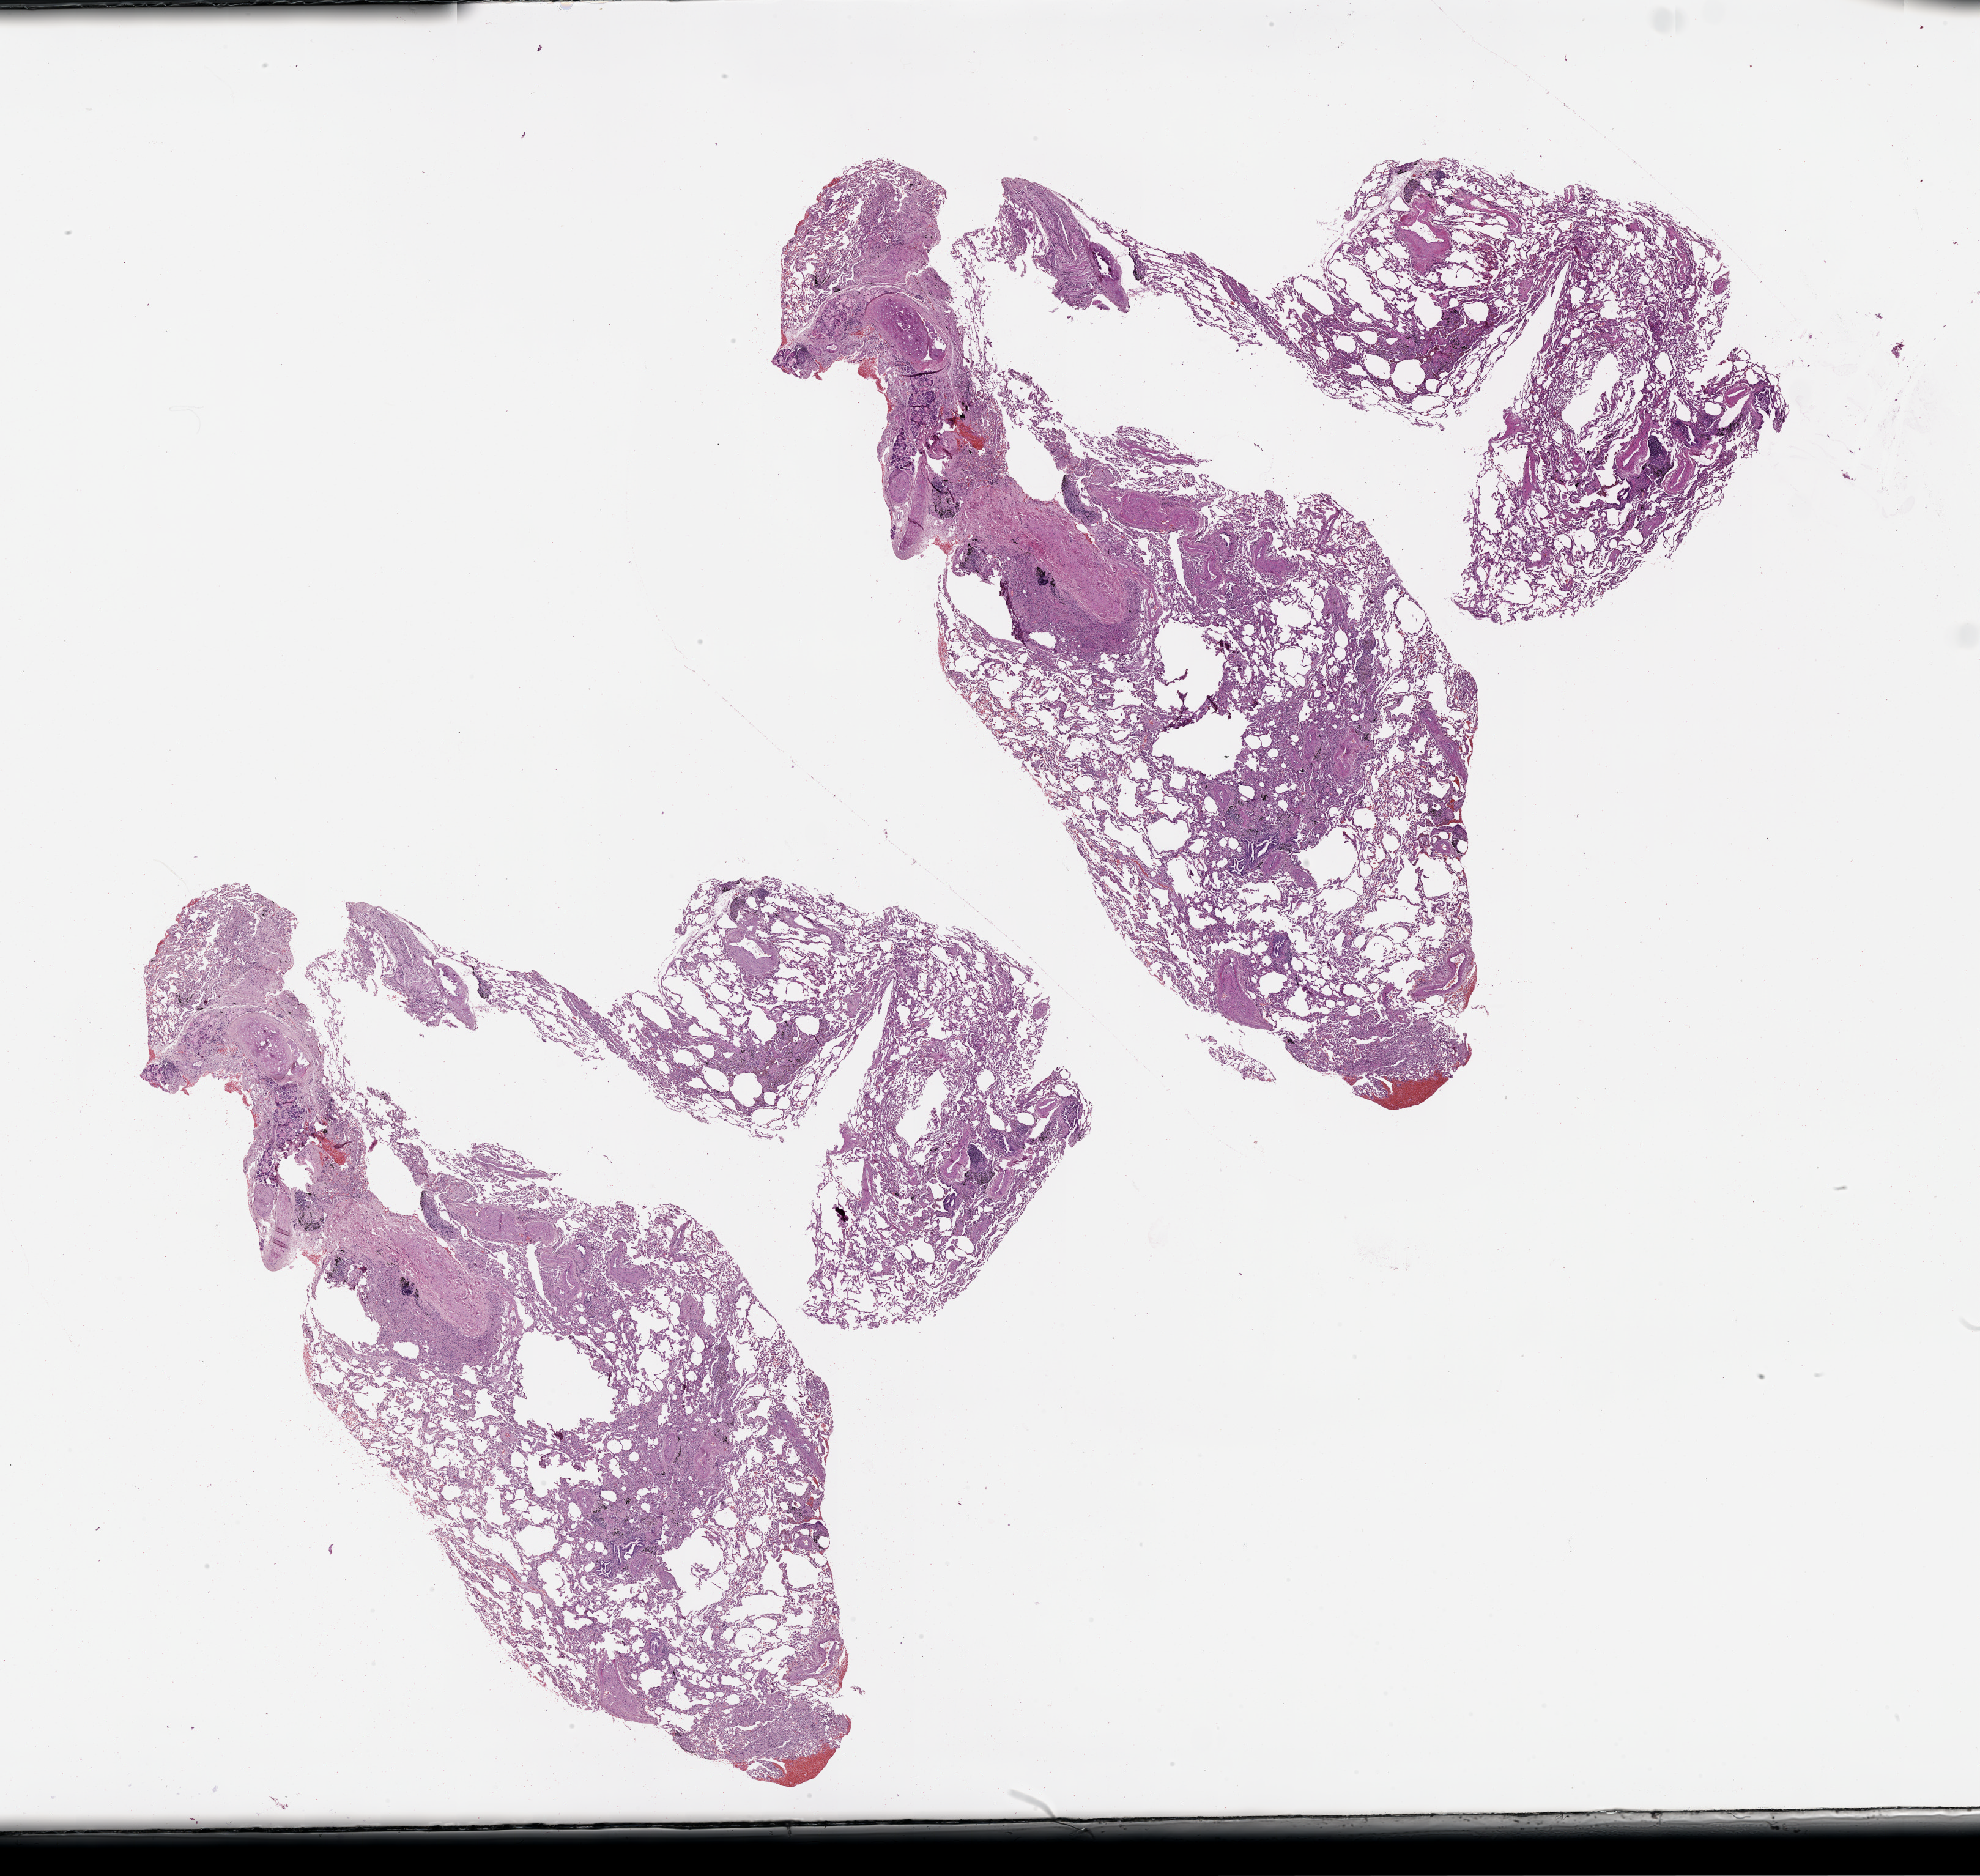
Digitized H&E-stained tissue section (whole slide) — whole scanned area (about 26.1 x 24.7 mm) shown as a low-resolution overview, normal (non-tumour) tissue sample, lung. Patient: female, age 60 years.
This section: normal (non-tumour) tissue from the same patient. Patient diagnosis (cohort enrolment): squamous cell carcinoma (lung).